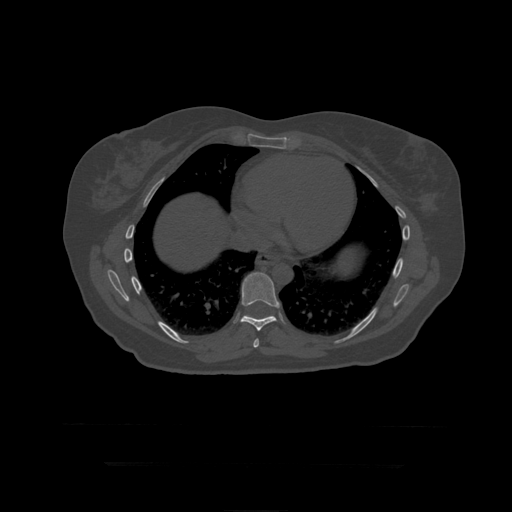
CT including the spine, one axial slice. Position 259 of 399 along the scan axis. 120 kVp. Bone window (W 1800 / L 400 HU). 1.25 mm slice thickness. 512 × 512 image matrix. Patient age 41 years. From the clinical record (not read from this slice): primary cancer: breast.
Structures marked on this image (semi-automatically segmented with operator editing):
- T10 vertebra: bounding box (x1, y1, x2, y2) in pixels: (246, 315, 273, 319)
- T8 vertebra: (253, 339, 259, 348)
- T9 vertebra: (241, 273, 280, 331)